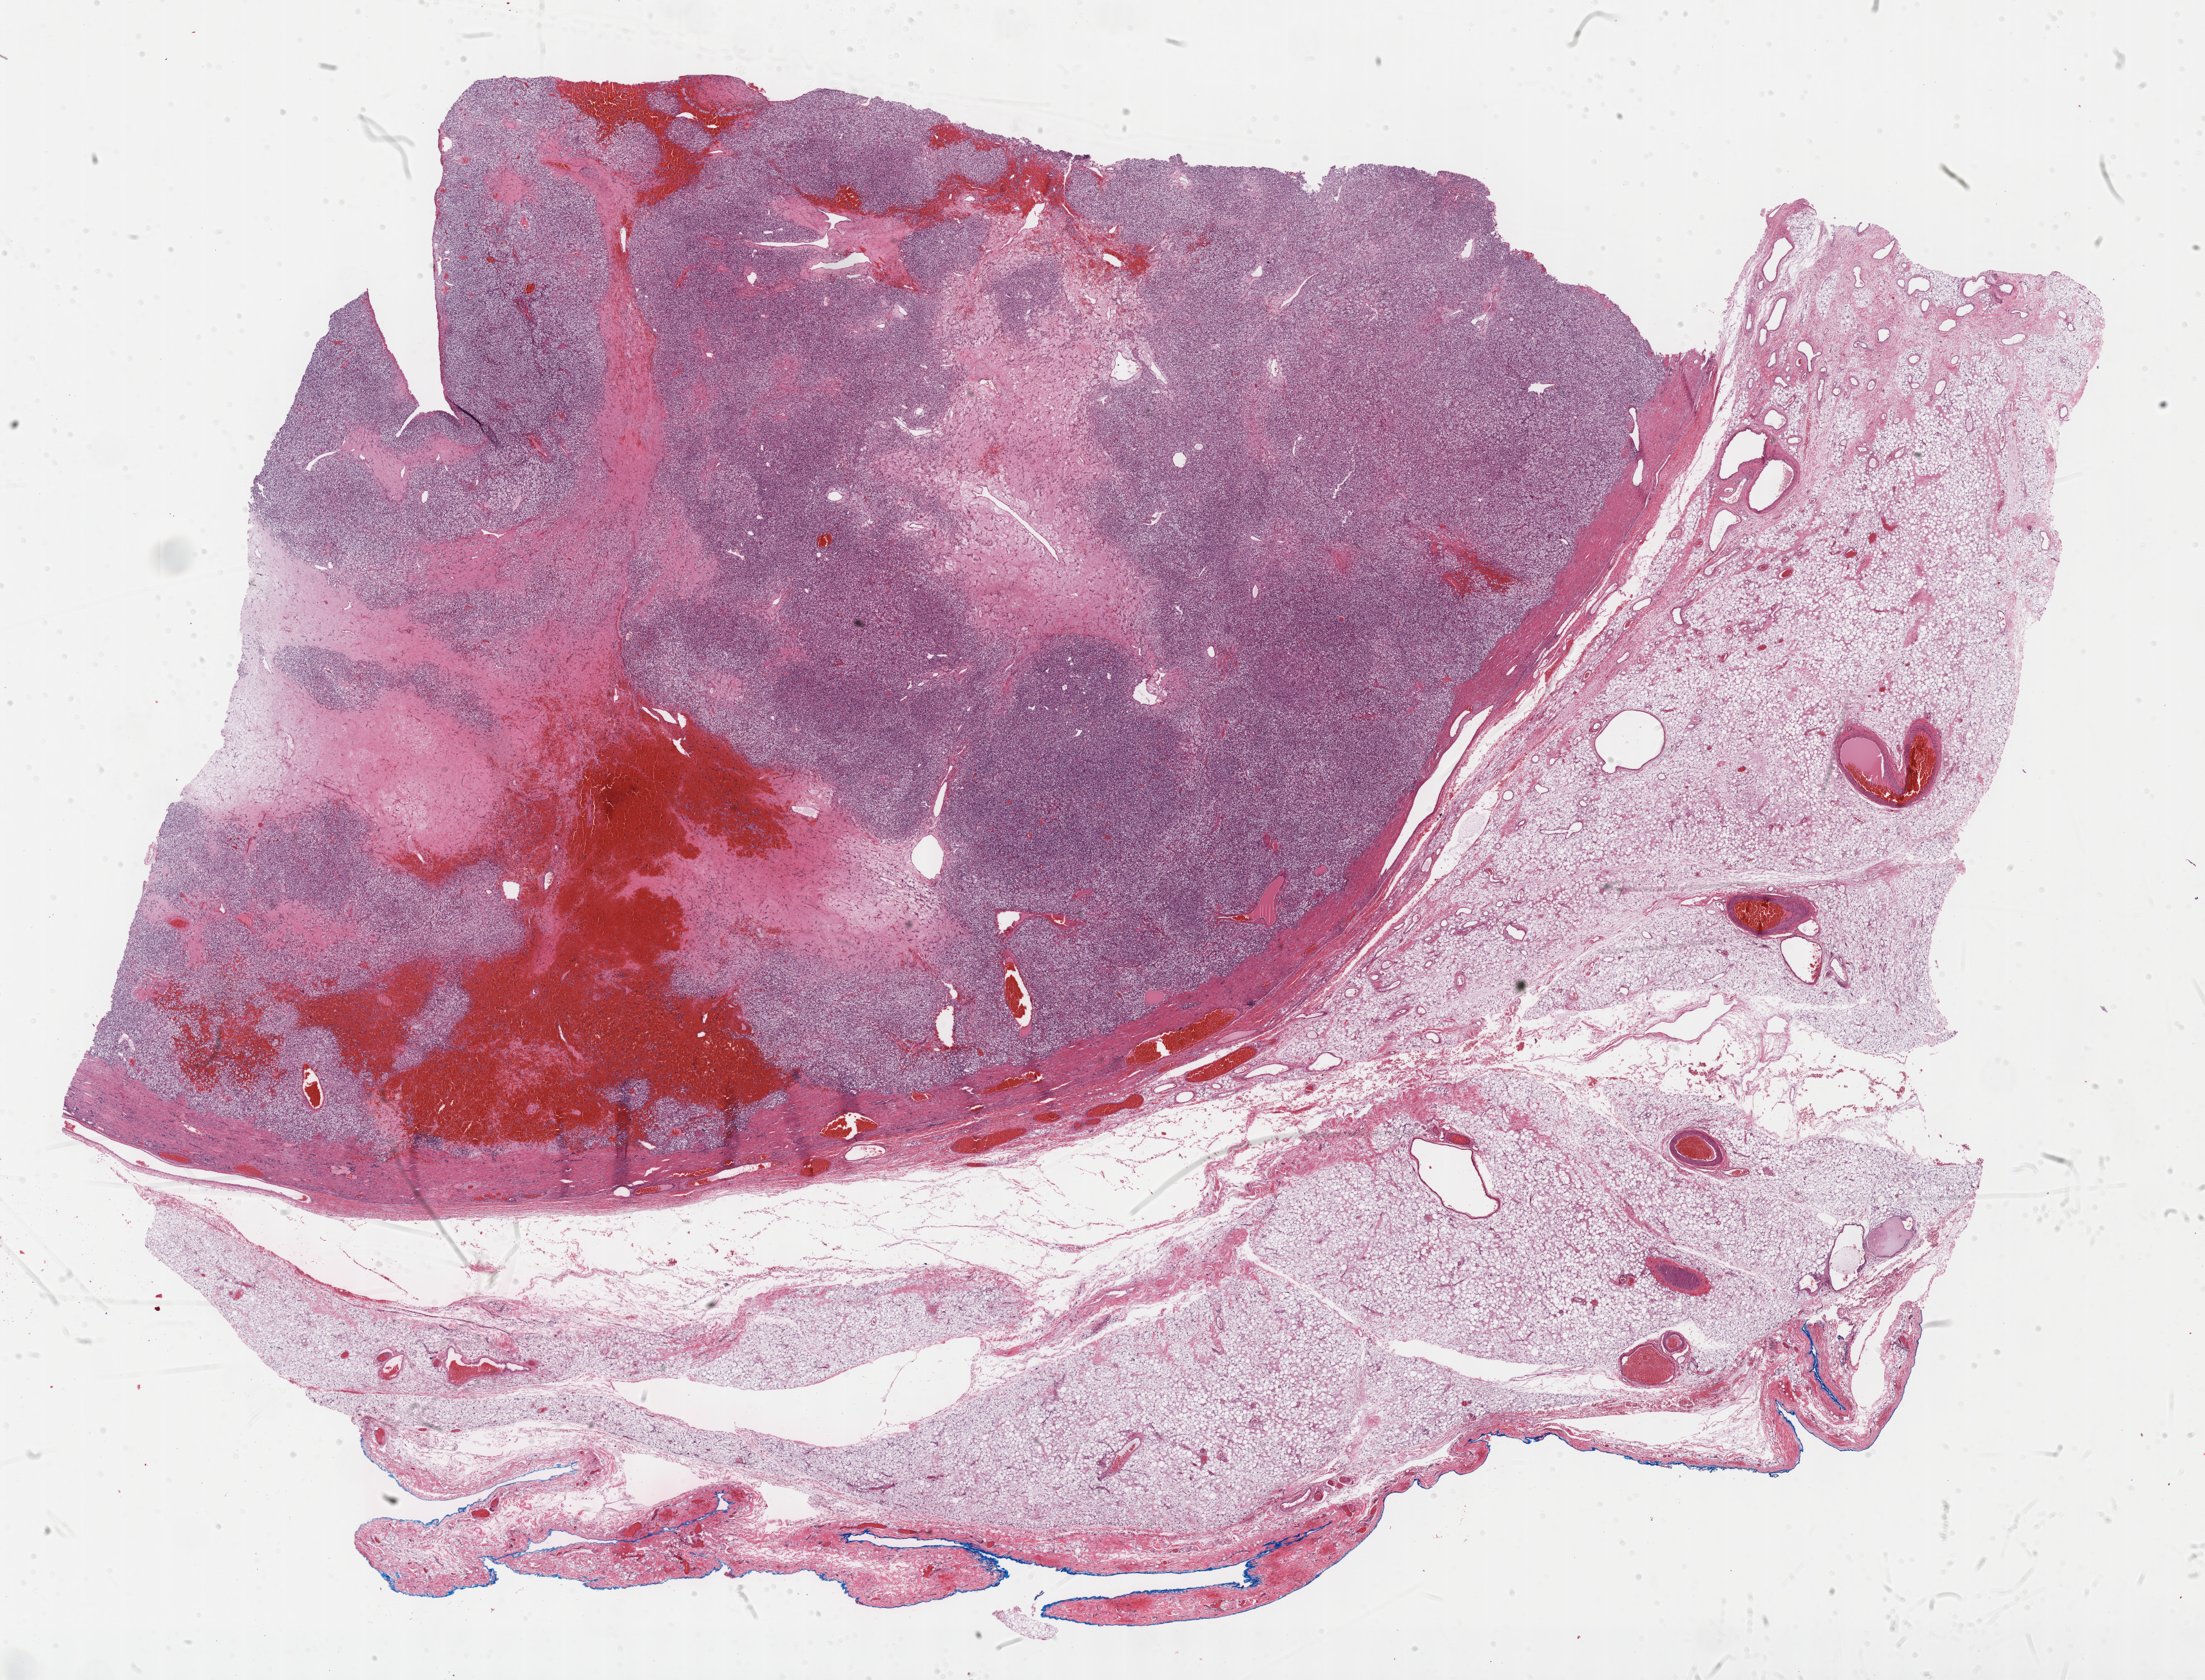
H&E whole-slide image, a low-resolution overview of the entire scanned area, about 27.7 x 21.1 mm (slide scanned at 40x); FFPE section; primary tumour sample from the kidney. Male, age 69 years at initial diagnosis. Histologic grade: G2 (moderately differentiated).
• AJCC pathologic stage: I (7th edition)
• histologic diagnosis: Clear cell adenocarcinoma, NOS
• TNM: T1a N0 M0